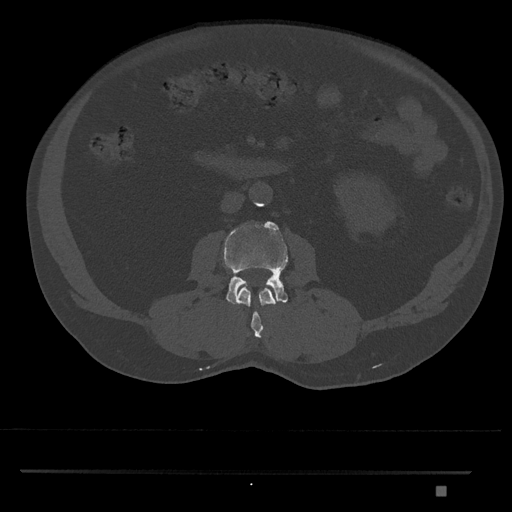
CT including the spine, one axial slice. Slice 711 of 1134 in the series (ordered by position). 120 kVp. Bone window (W 1800 / L 400 HU). 0.5 mm slice thickness. 512 × 512 image matrix, field of view 429 × 429 mm. Male patient, age 65 years. From the clinical record (not read from this slice): primary cancer: prostate.
Structures marked on this image (semi-automatically segmented with operator editing):
- L2 vertebra: box from (x=237, y=286) to (x=276, y=338) px
- L3 vertebra: (x=223, y=221)–(x=288, y=306)